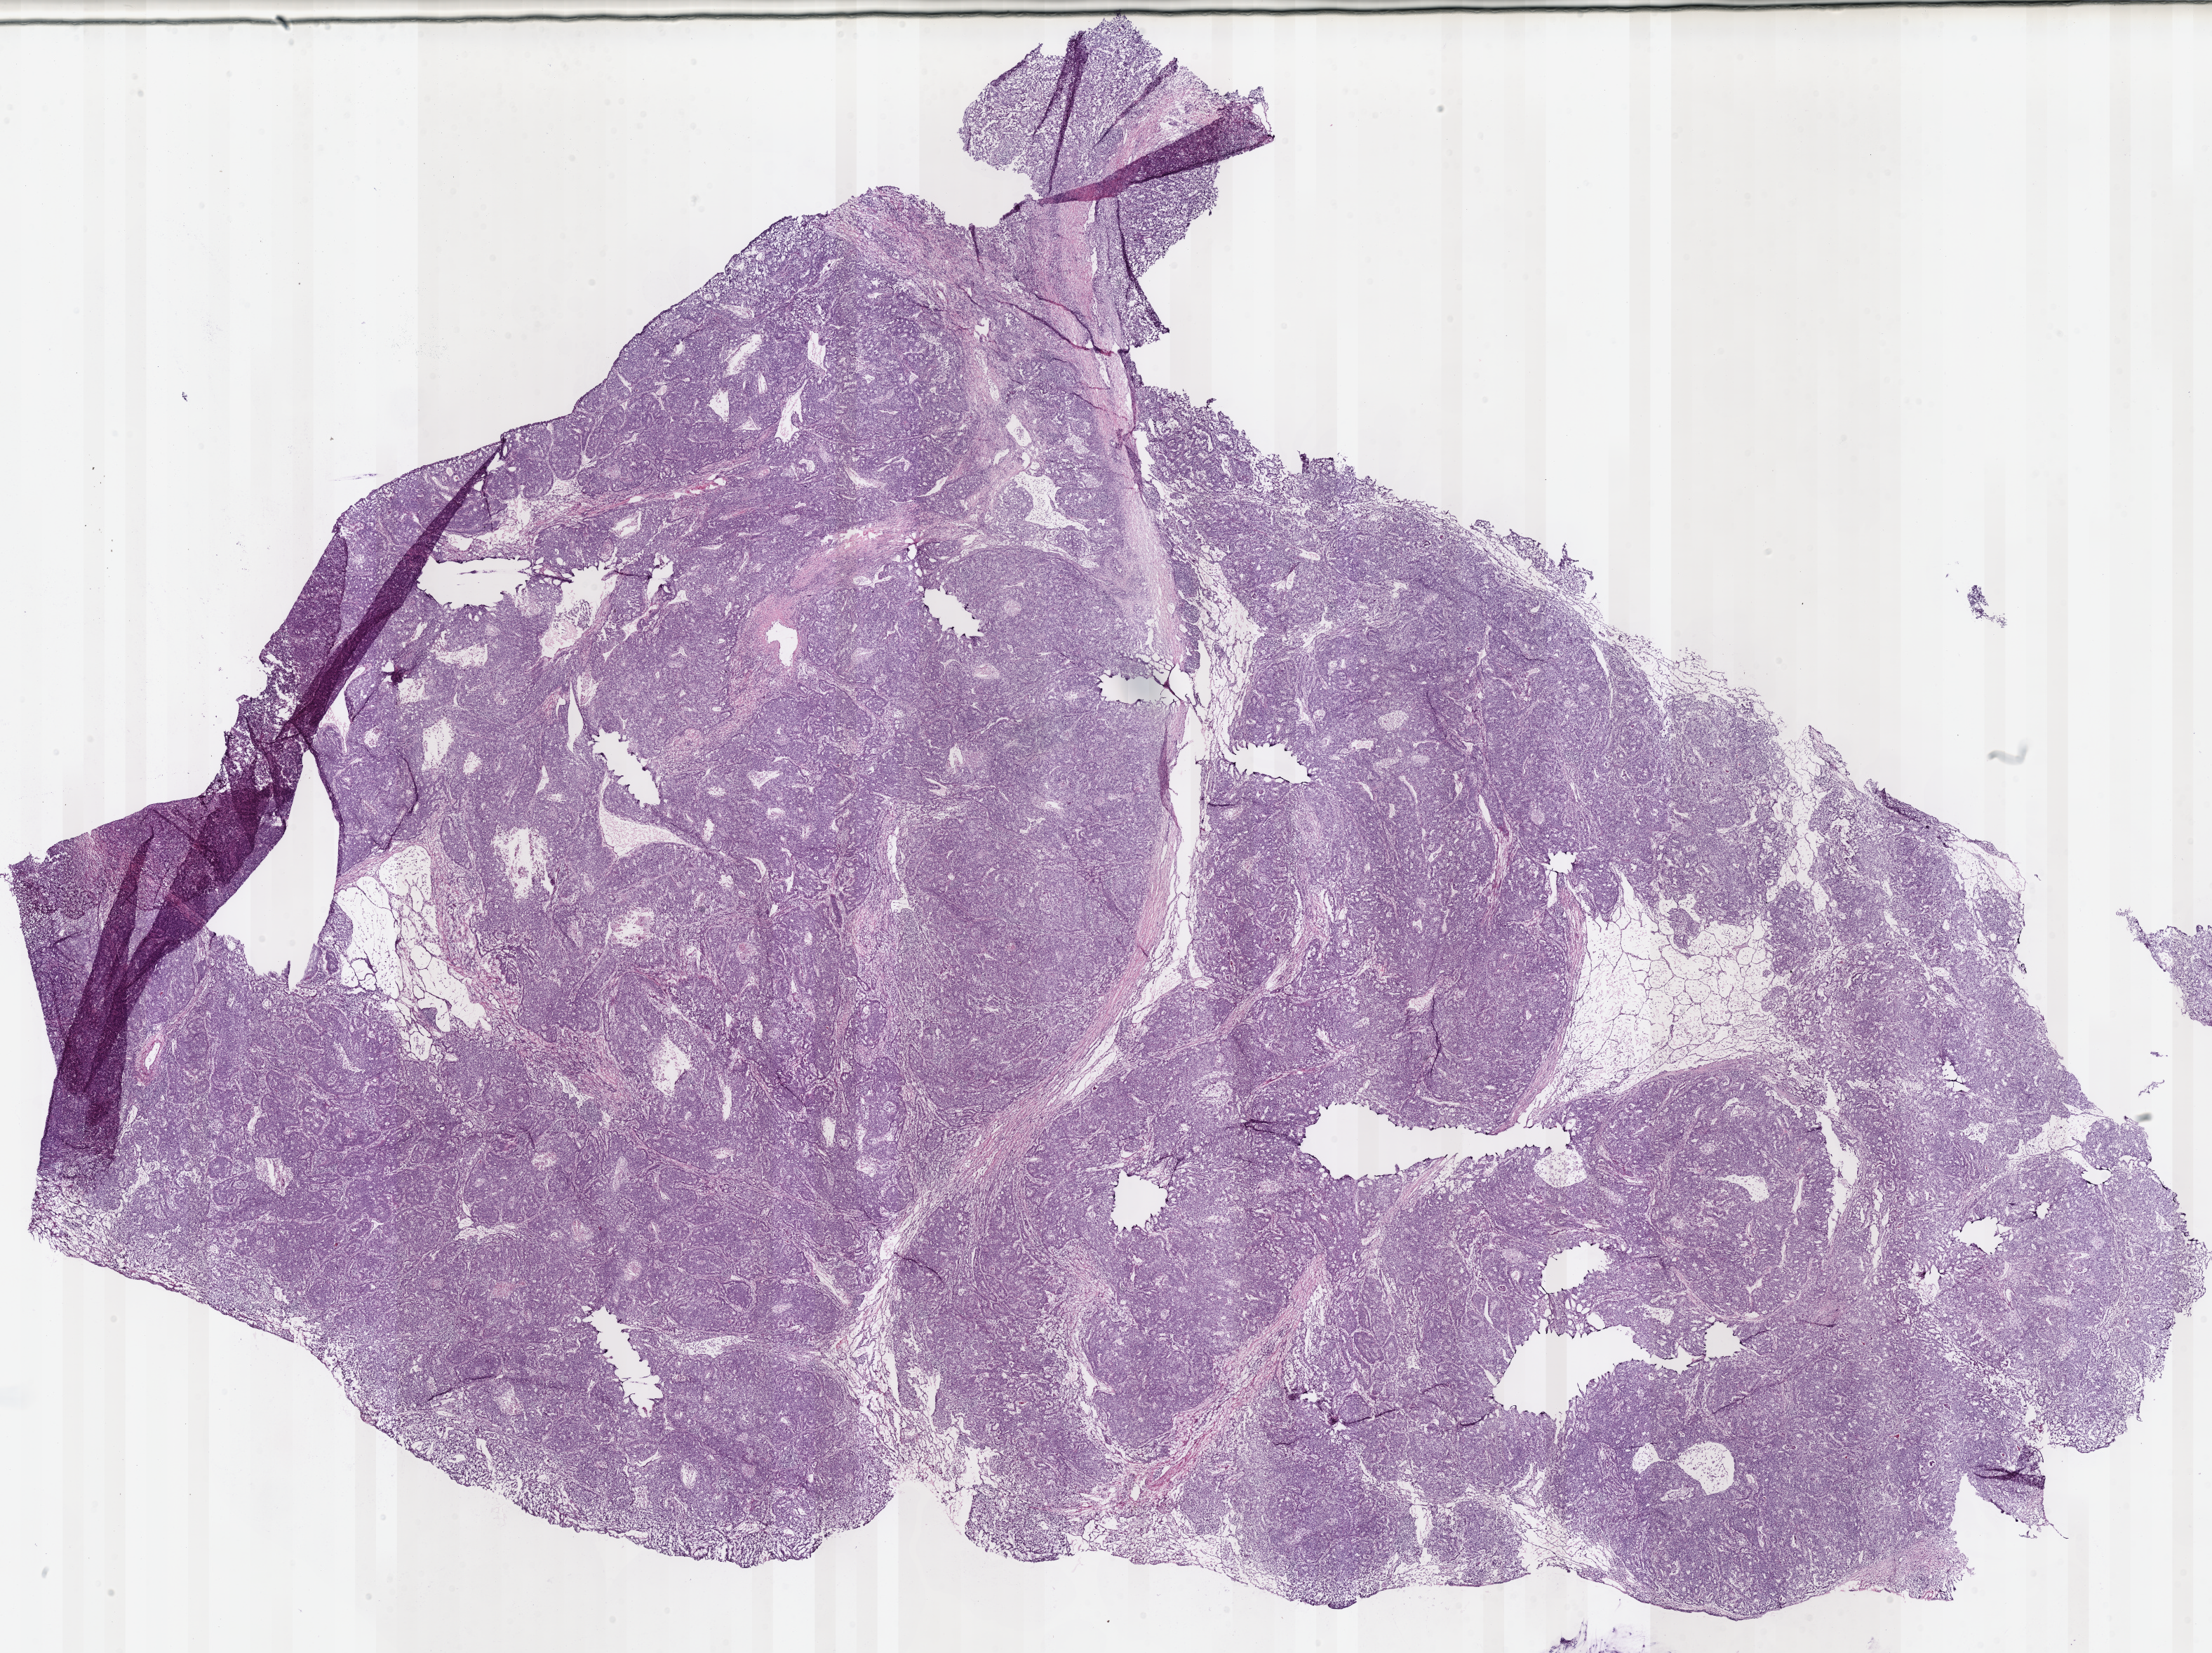
Digitized Hematoxylin and eosin (H&E) stained tissue section (whole slide), a low-resolution overview of the entire scanned area, about 24.8 x 18.6 mm (from a 40x scan); frozen section from the bottom of the tissue portion; sample: primary tumour, lung. Male, age 64 years at initial diagnosis. Slide review estimates, as recorded: tumour cells 100%, tumour nuclei 80%, normal cells 0%, stromal cells 0%, necrosis 0%. Infiltration values recorded for this section: lymphocyte infiltration 10%, monocyte infiltration 0%, neutrophil infiltration 0%.
Diagnosis: Adenocarcinoma, NOS (upper lobe, lung). Laterality: right. AJCC pathologic stage: IA (7th edition).